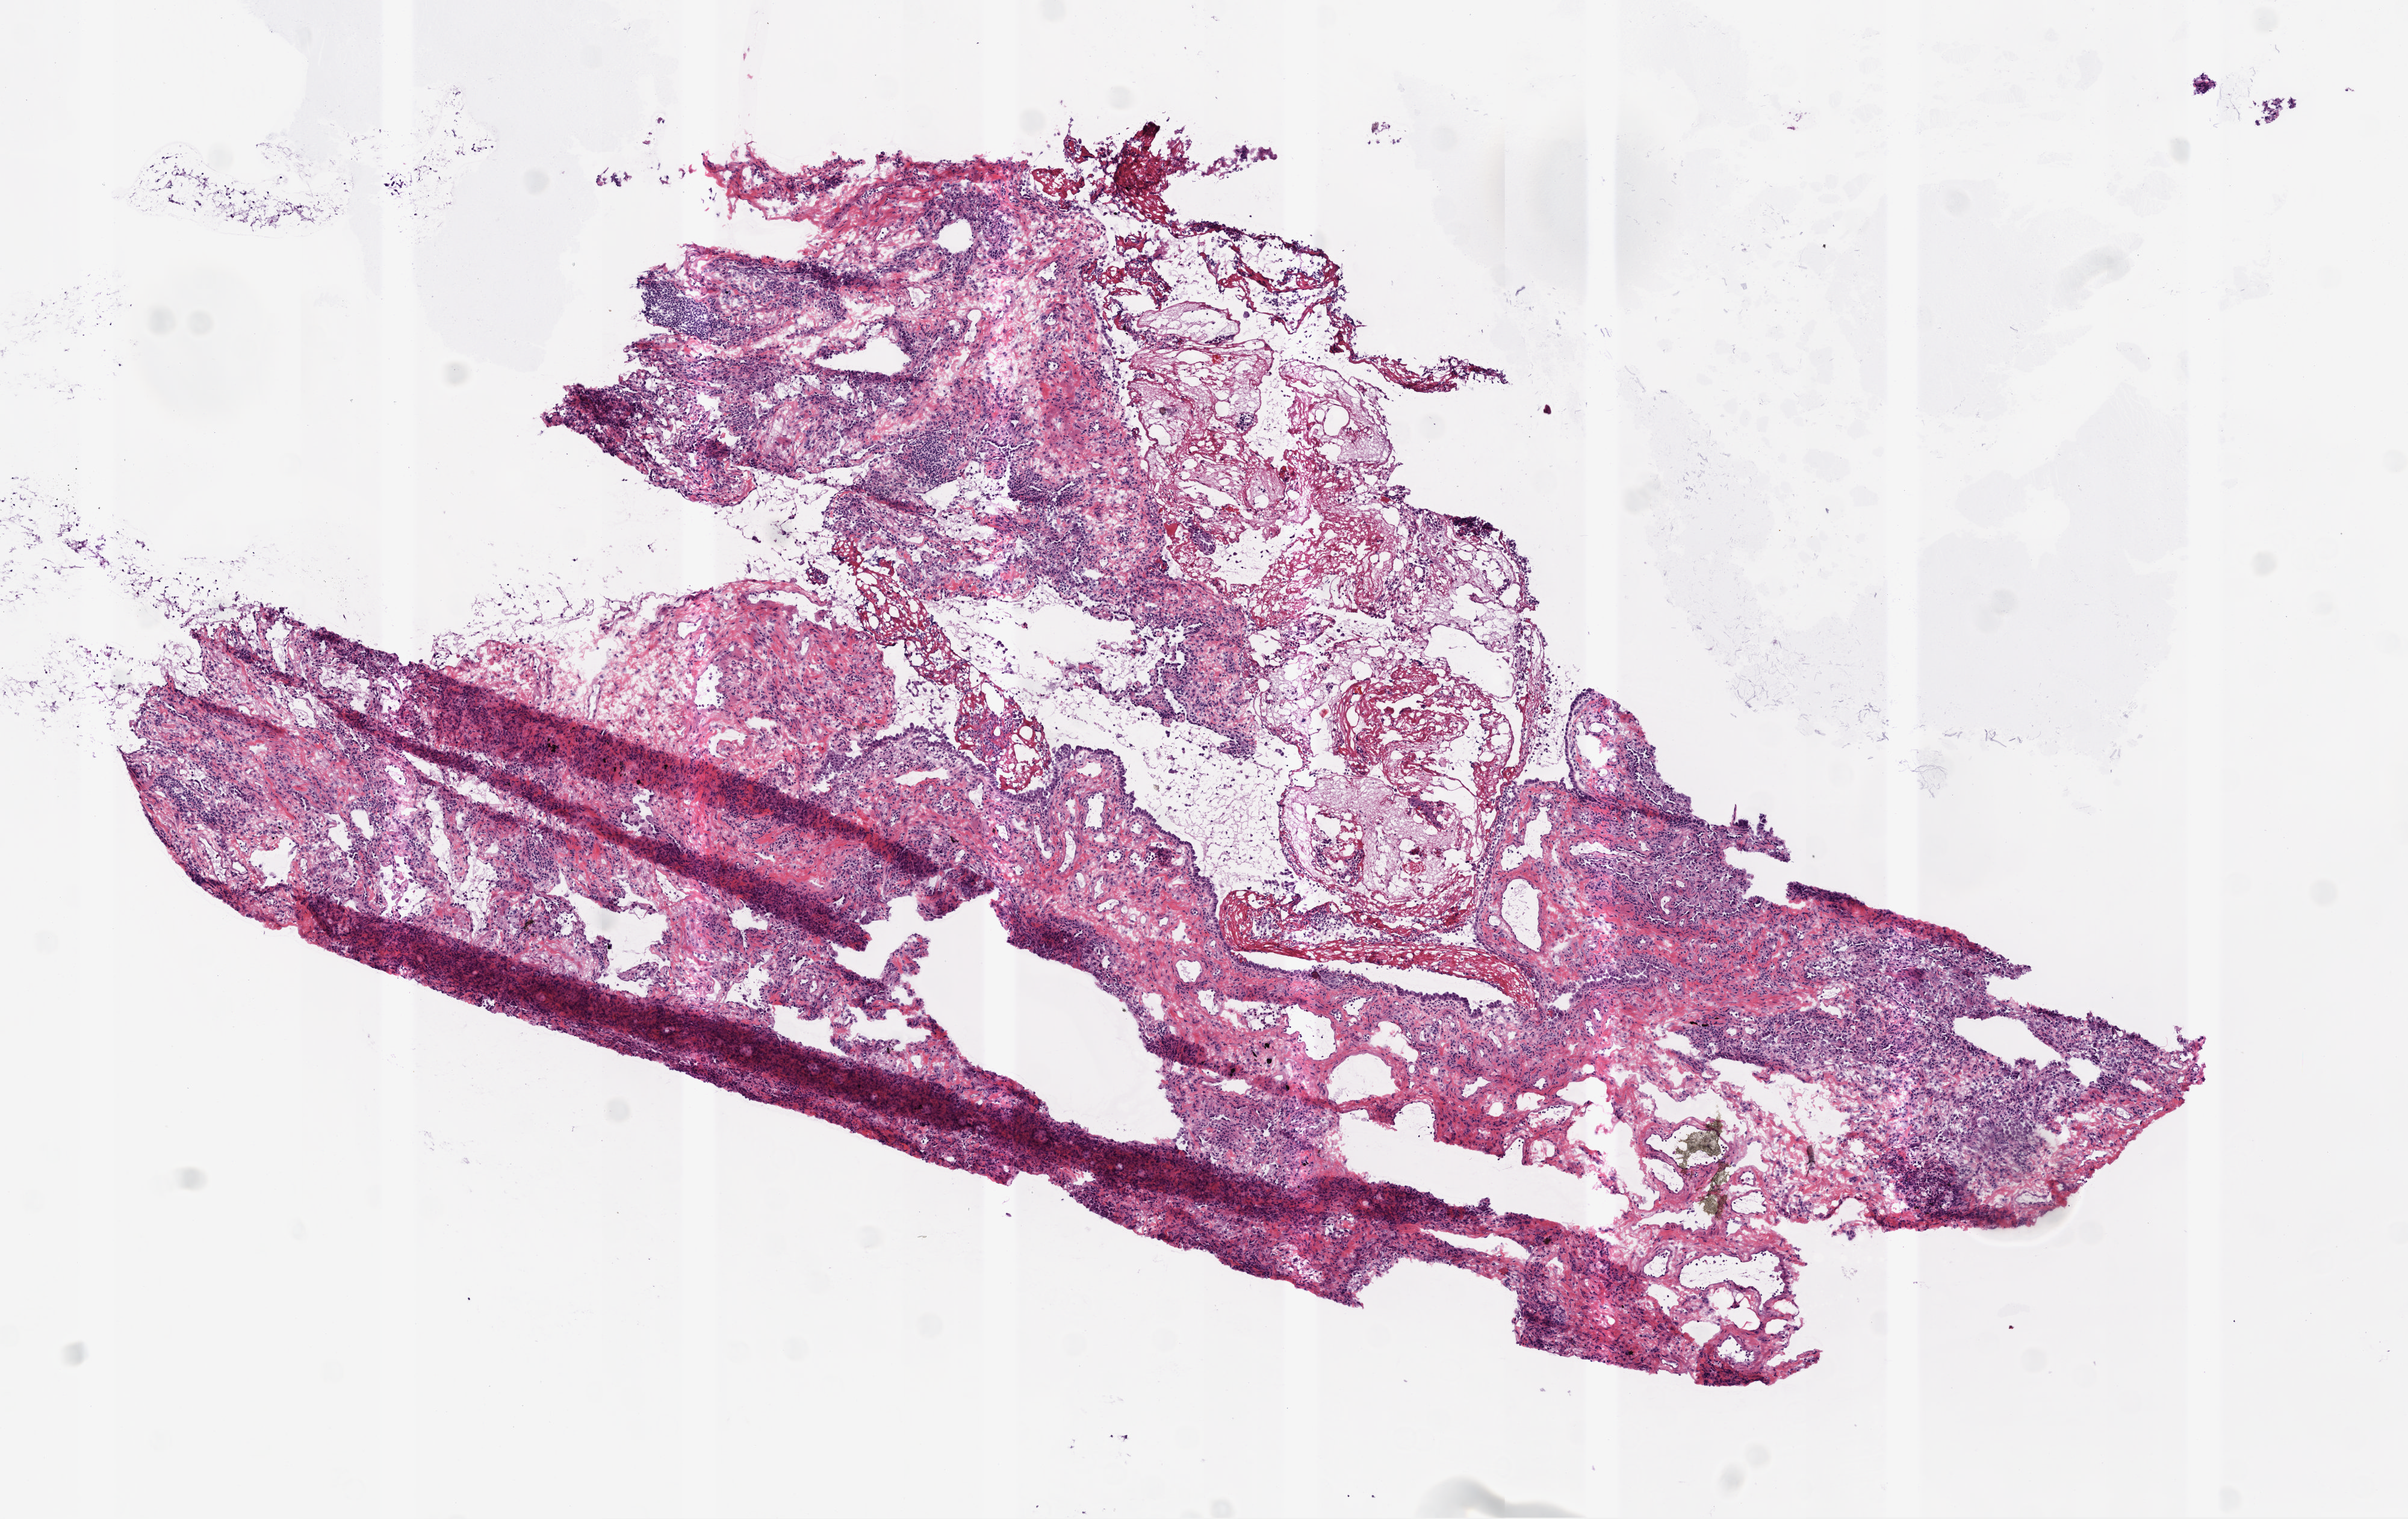
H&E-stained whole-slide image, shown as a low-resolution overview of the whole scanned area (about 8.0 x 5.1 mm); frozen section from the top of the tissue portion; sample: solid tissue normal (non-tumour tissue), lung. Male, age 75 years at initial diagnosis.
- this section: solid tissue normal sample (biorepository sample class)
- patient diagnosis: Squamous cell carcinoma, NOS (upper lobe, lung)